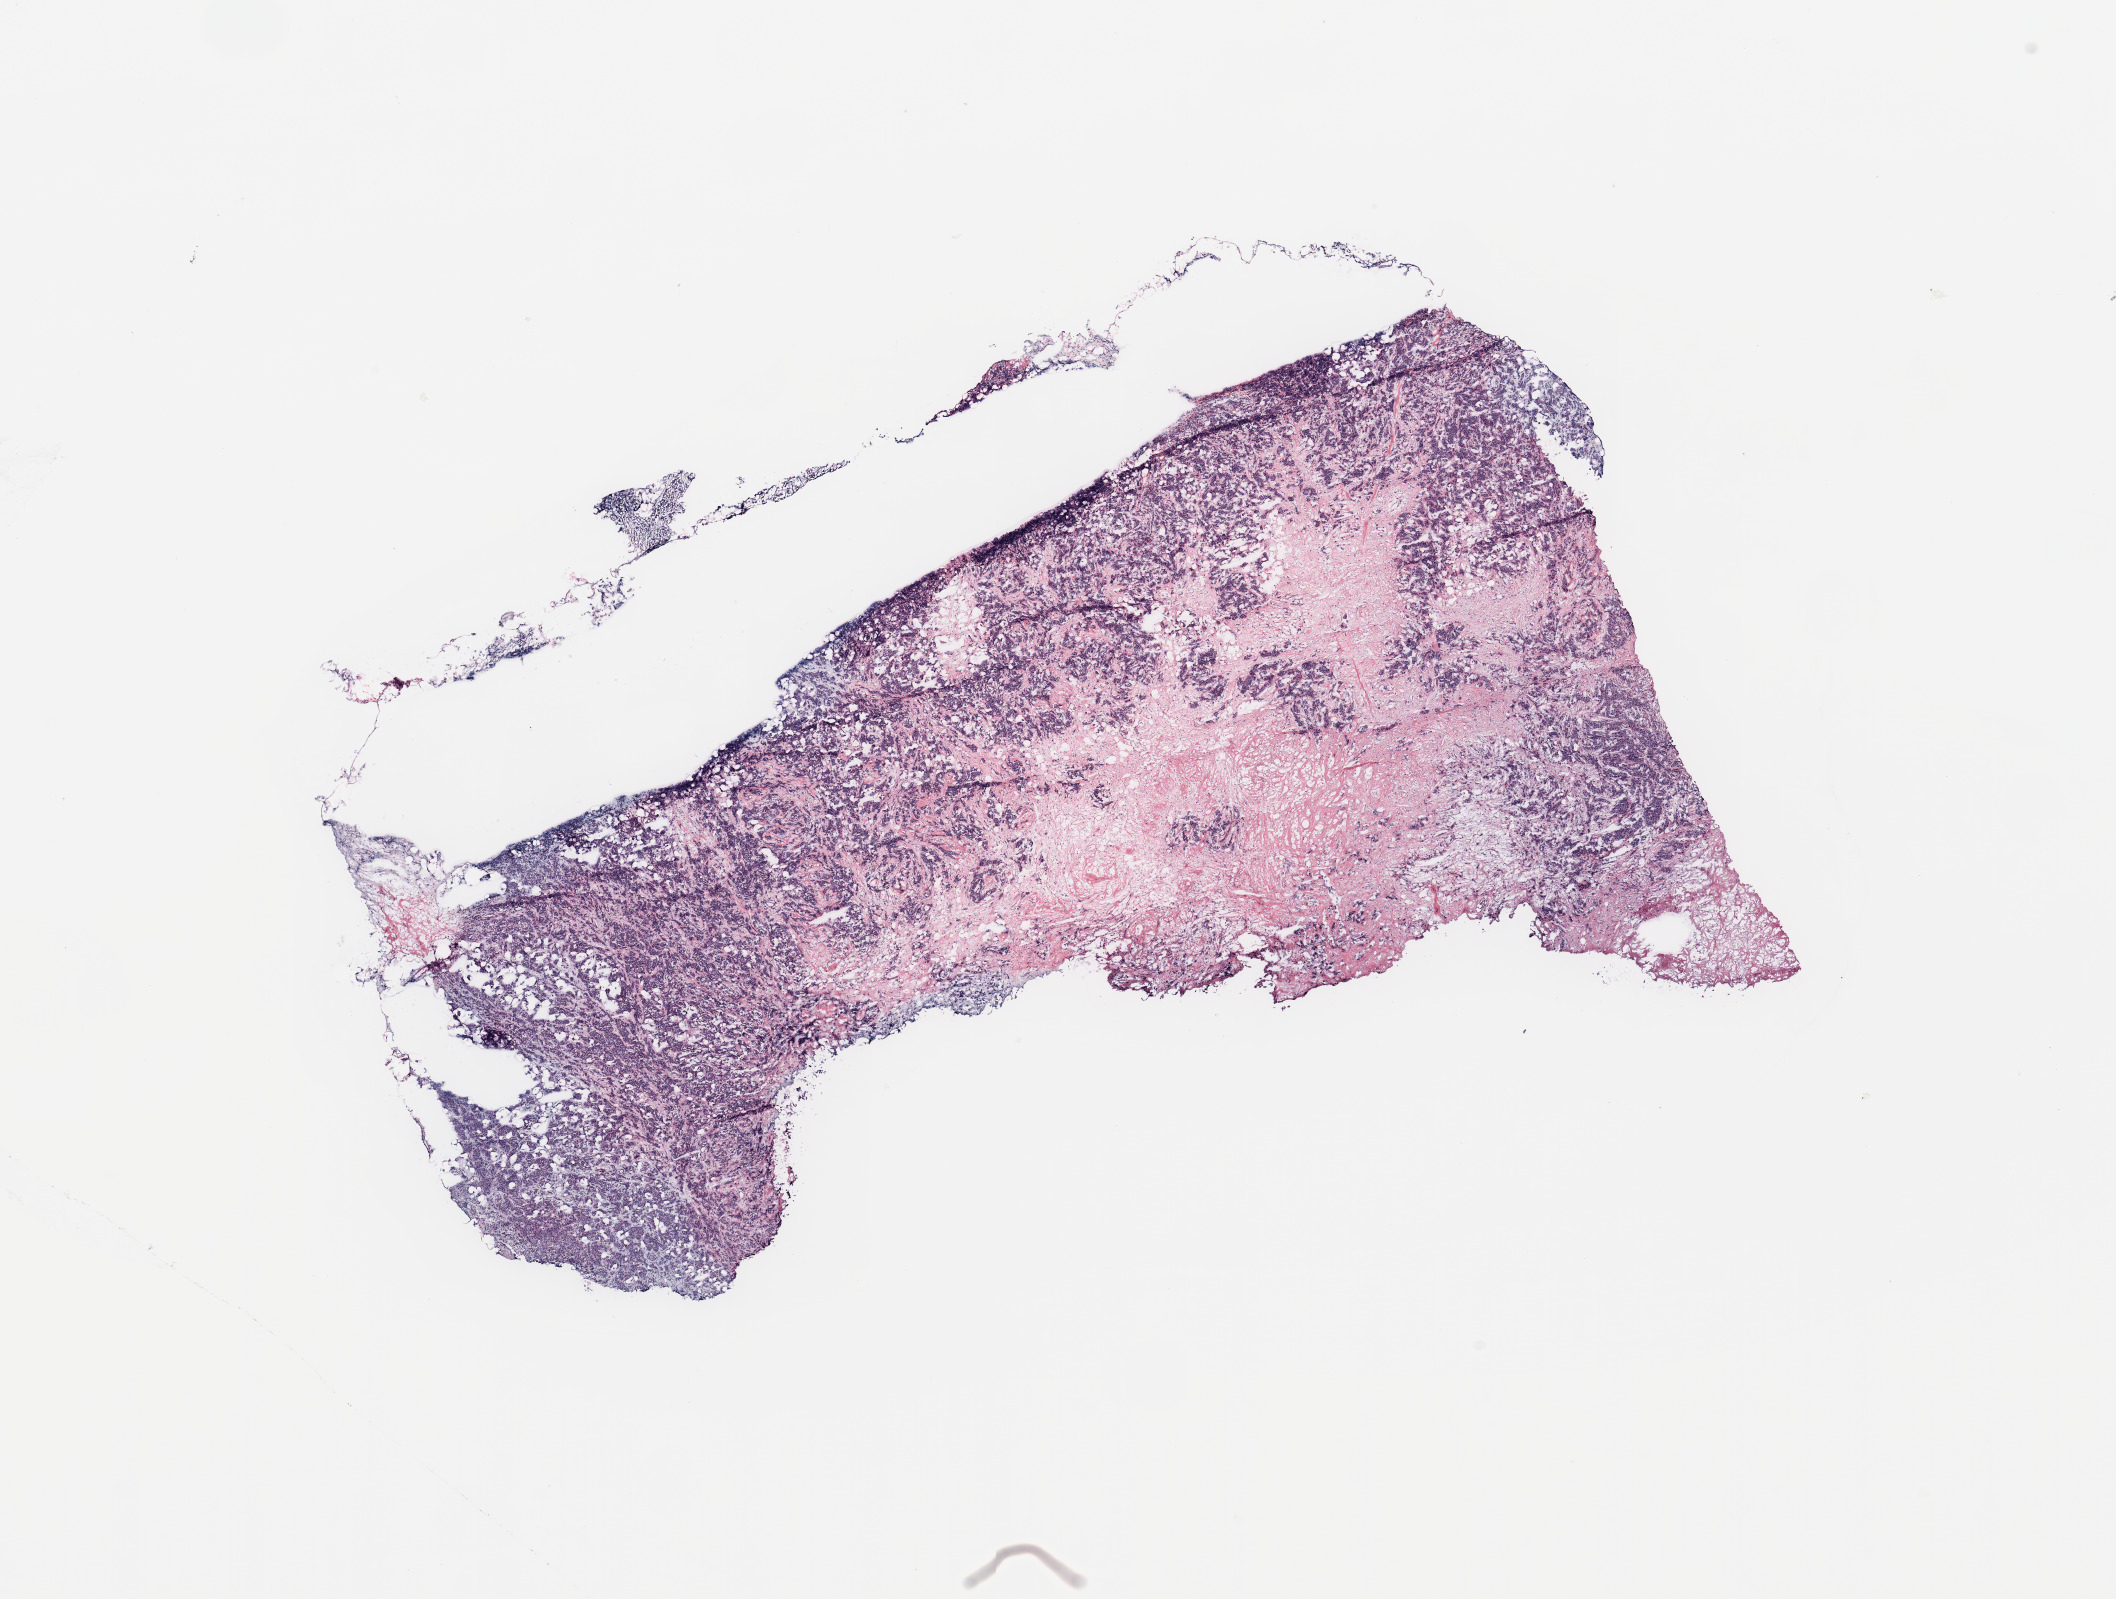
Whole-slide histology image, H&E-stained, low-resolution overview of the scanned area, about 16.7 x 12.6 mm, breast, tumour tissue. Female, 60 y/o.
• AJCC pathologic stage: IIA
• diagnosis: Infiltrating duct carcinoma, NOS